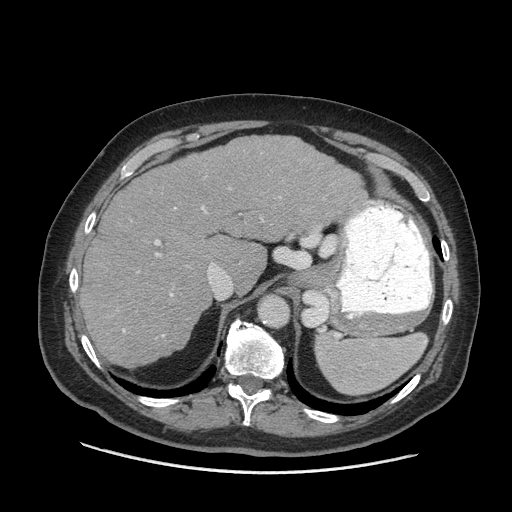
Contrast-enhanced abdominal CT (liver protocol), one axial slice; position 48 of 77 along the scan axis; reconstruction kernel STANDARD; soft-tissue window (W 400 / L 40 HU); 2.5 mm slice thickness; 512 × 512 image matrix. Case-level facts recorded for this patient, not image findings: diagnosis: hepatocellular carcinoma (patient treated with transarterial chemoembolisation; whether this scan precedes or follows treatment is not stated here); TNM stage (as recorded): Stage-I; Child-Pugh class: A; tumour size: 3.8 cm.
Structures marked on this image (semi-automatically segmented with operator editing):
- liver parenchyma outside the tumour (the mass and vessels are separate outlines, so this box may not span the whole liver): bounding box (x1, y1, x2, y2) in pixels: (82, 136, 366, 366)
- liver vessels: (123, 197, 281, 336)